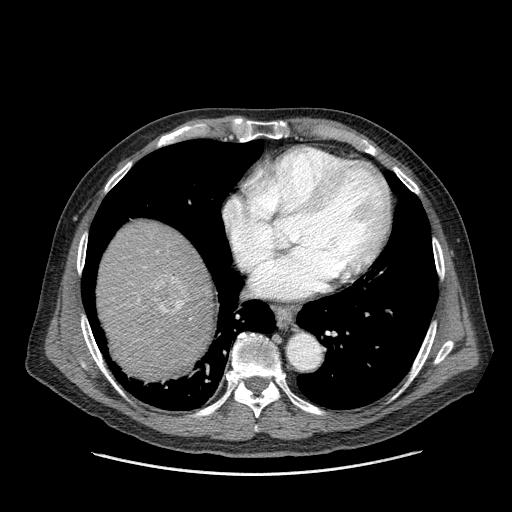
Contrast-enhanced abdominal CT (liver protocol), one axial slice. Slice 146 of 180 in the series (ordered by position). Reconstruction kernel STANDARD. One of 2 acquisitions stored at this slice position. Soft-tissue window (W 400 / L 40 HU). 512 × 512 image matrix. From the clinical record (not read from this slice): diagnosis: hepatocellular carcinoma (patient treated with transarterial chemoembolisation; whether this scan precedes or follows treatment is not stated here); TNM stage (as recorded): Stage-II; Child-Pugh class: A; tumour differentiation: well differentiated.
Structures marked on this image (semi-automatic segmentation, software-assisted and operator-edited):
- liver parenchyma outside the tumour (the mass and vessels are separate outlines, so this box may not span the whole liver): bounding box [x1, y1, x2, y2] px = [98, 220, 214, 380]
- mass: [149, 273, 190, 315]